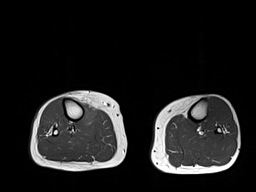
MRI of an extremity soft-tissue mass, one axial slice; 256 × 192 image matrix, field of view 375 × 281 mm. Female patient. From the clinical record (not read from this slice): histological type: undifferentiated – high grade; grade: high; site of the primary tumour: right thigh.
Annotated regions visible in this slice (expert manual segmentation):
- gross tumour volume (mass): bounding box [x1, y1, x2, y2] px = [82, 105, 98, 126]